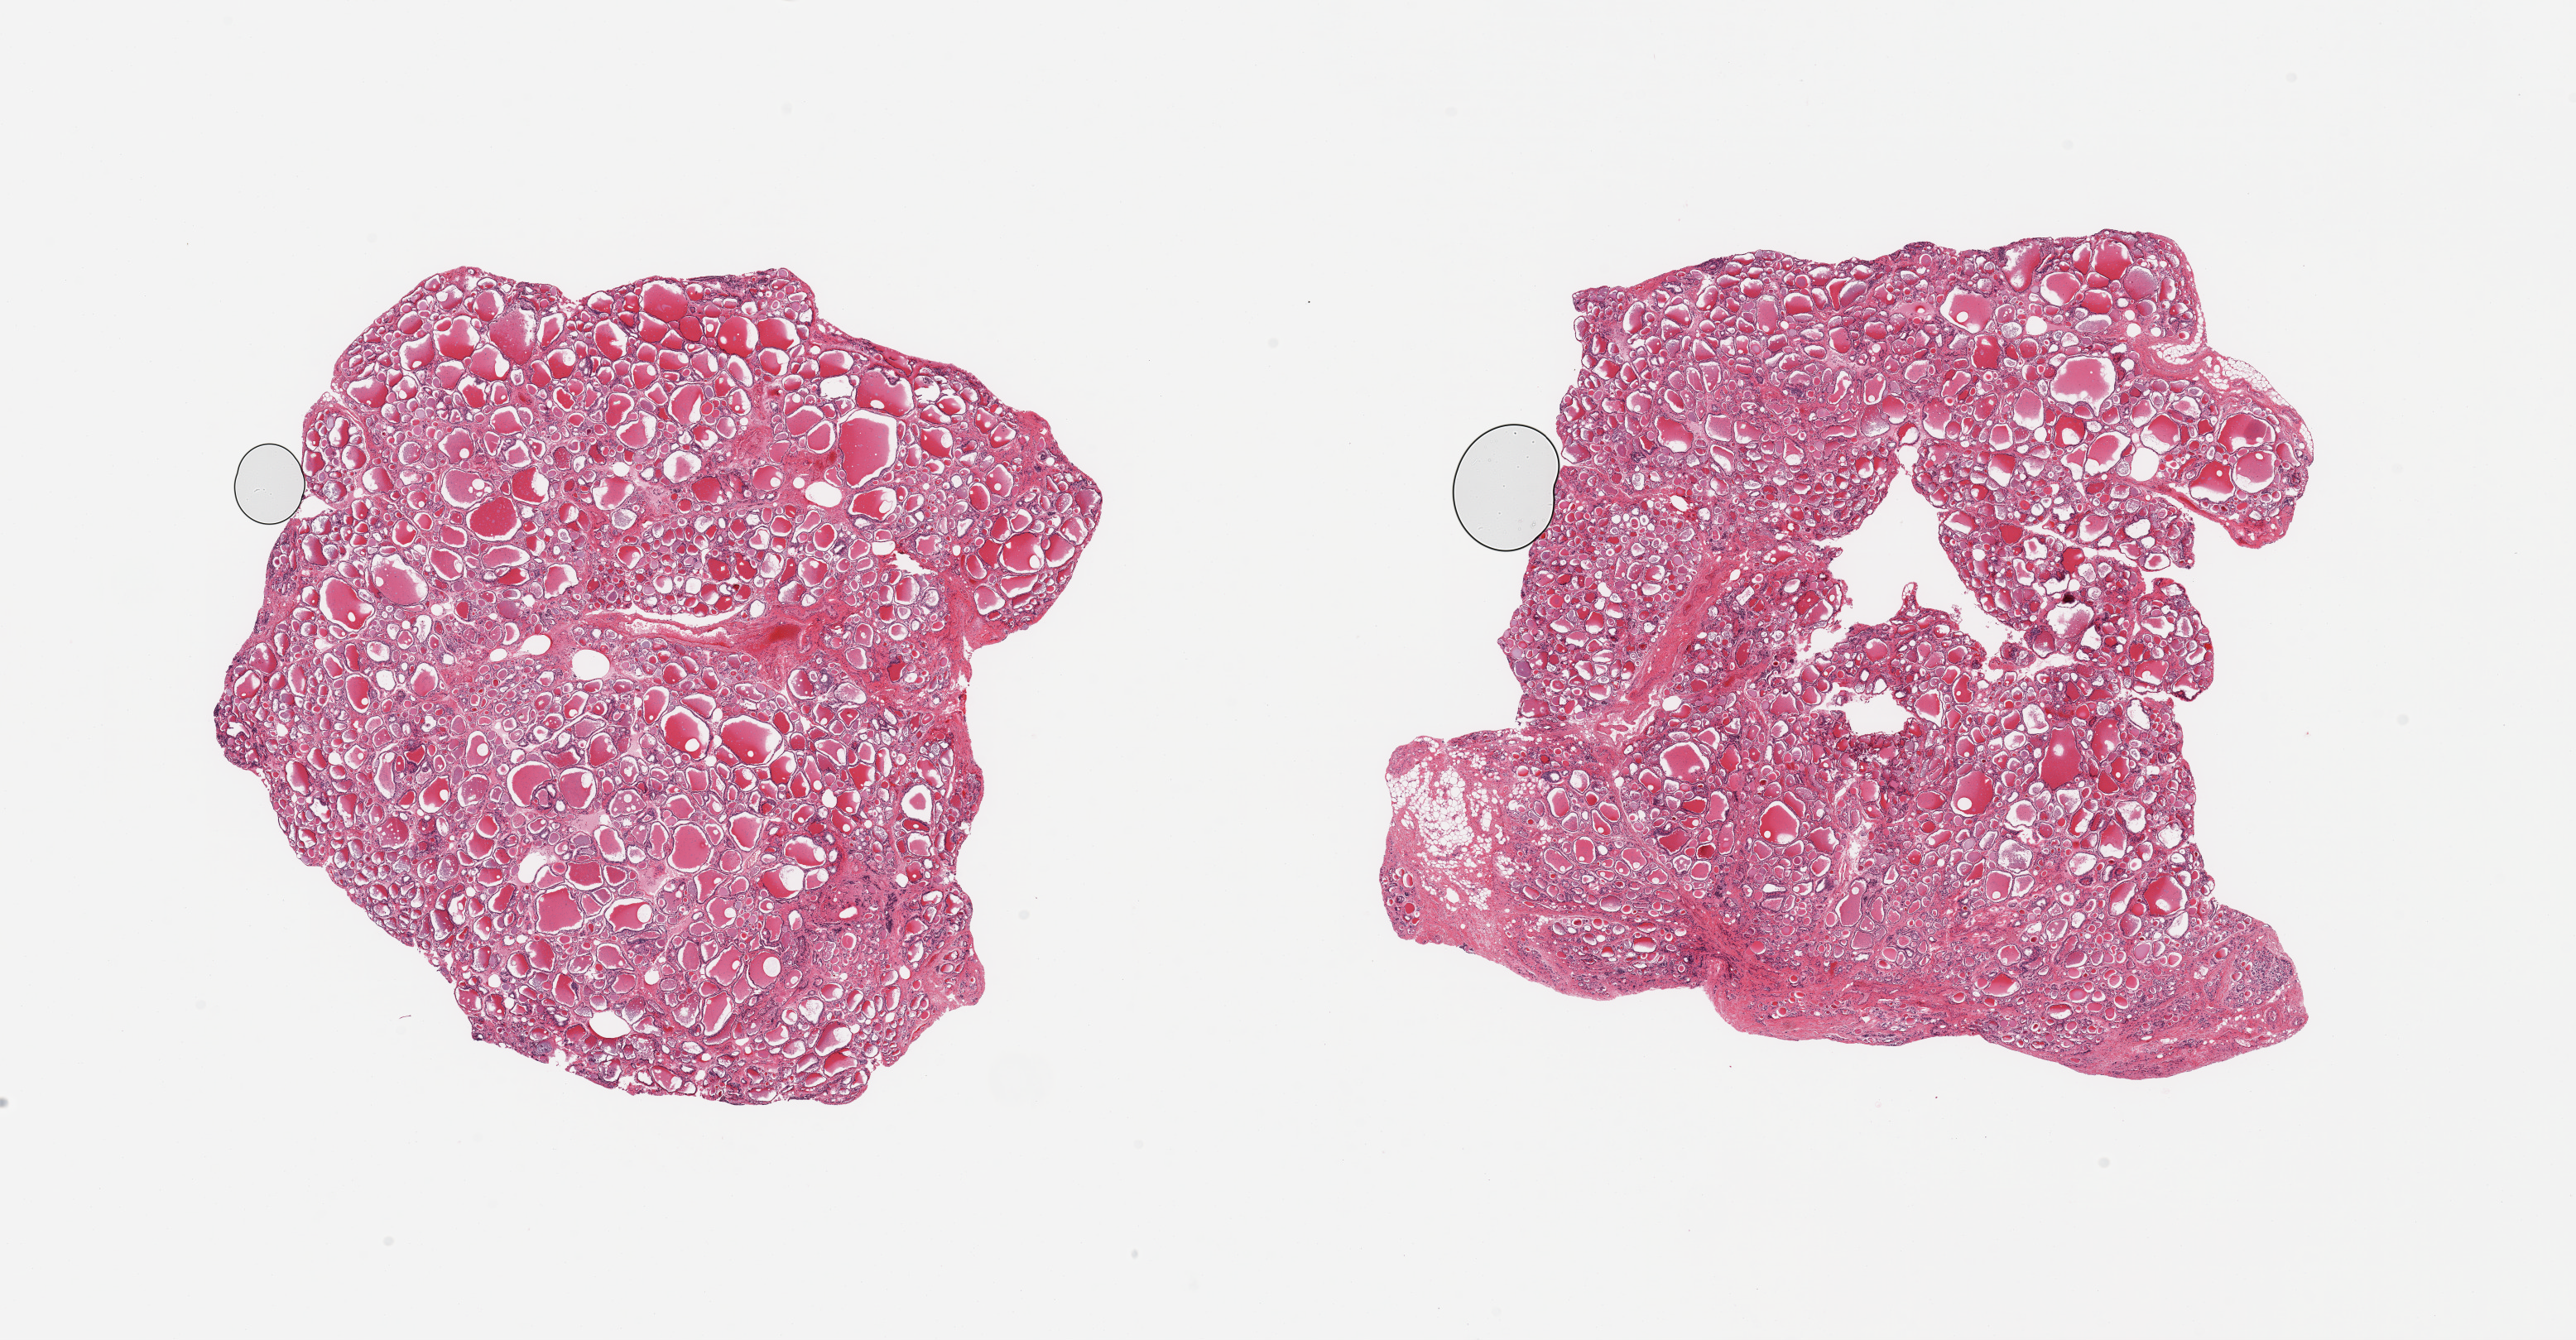
Digitized H&E-stained section — shown as a low-resolution overview of the whole scanned area (about 24.6 x 12.8 mm); PAXgene-fixed paraffin-embedded (PFPE) section; target tissue: thyroid; tissue donor sample.
• pathologist's review note for this sample: 2 pieces; <5% external fat